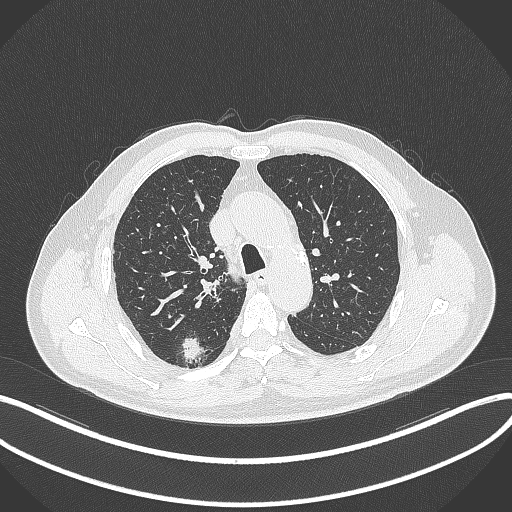
Chest CT, one axial slice. 120 kVp. Lung window (W 1500 / L -600 HU). 1 mm slice thickness. 512 × 512 image matrix. Male patient, age 69 years. Case-level facts recorded for this patient, not image findings: clinical TNM (as recorded): T1b N0 M0; histopathological grade: G2-3.
Structures marked on this image (bounding box drawn by a radiologist):
- lung tumour (recorded histology: adenocarcinoma): box from (x=182, y=331) to (x=206, y=362) px